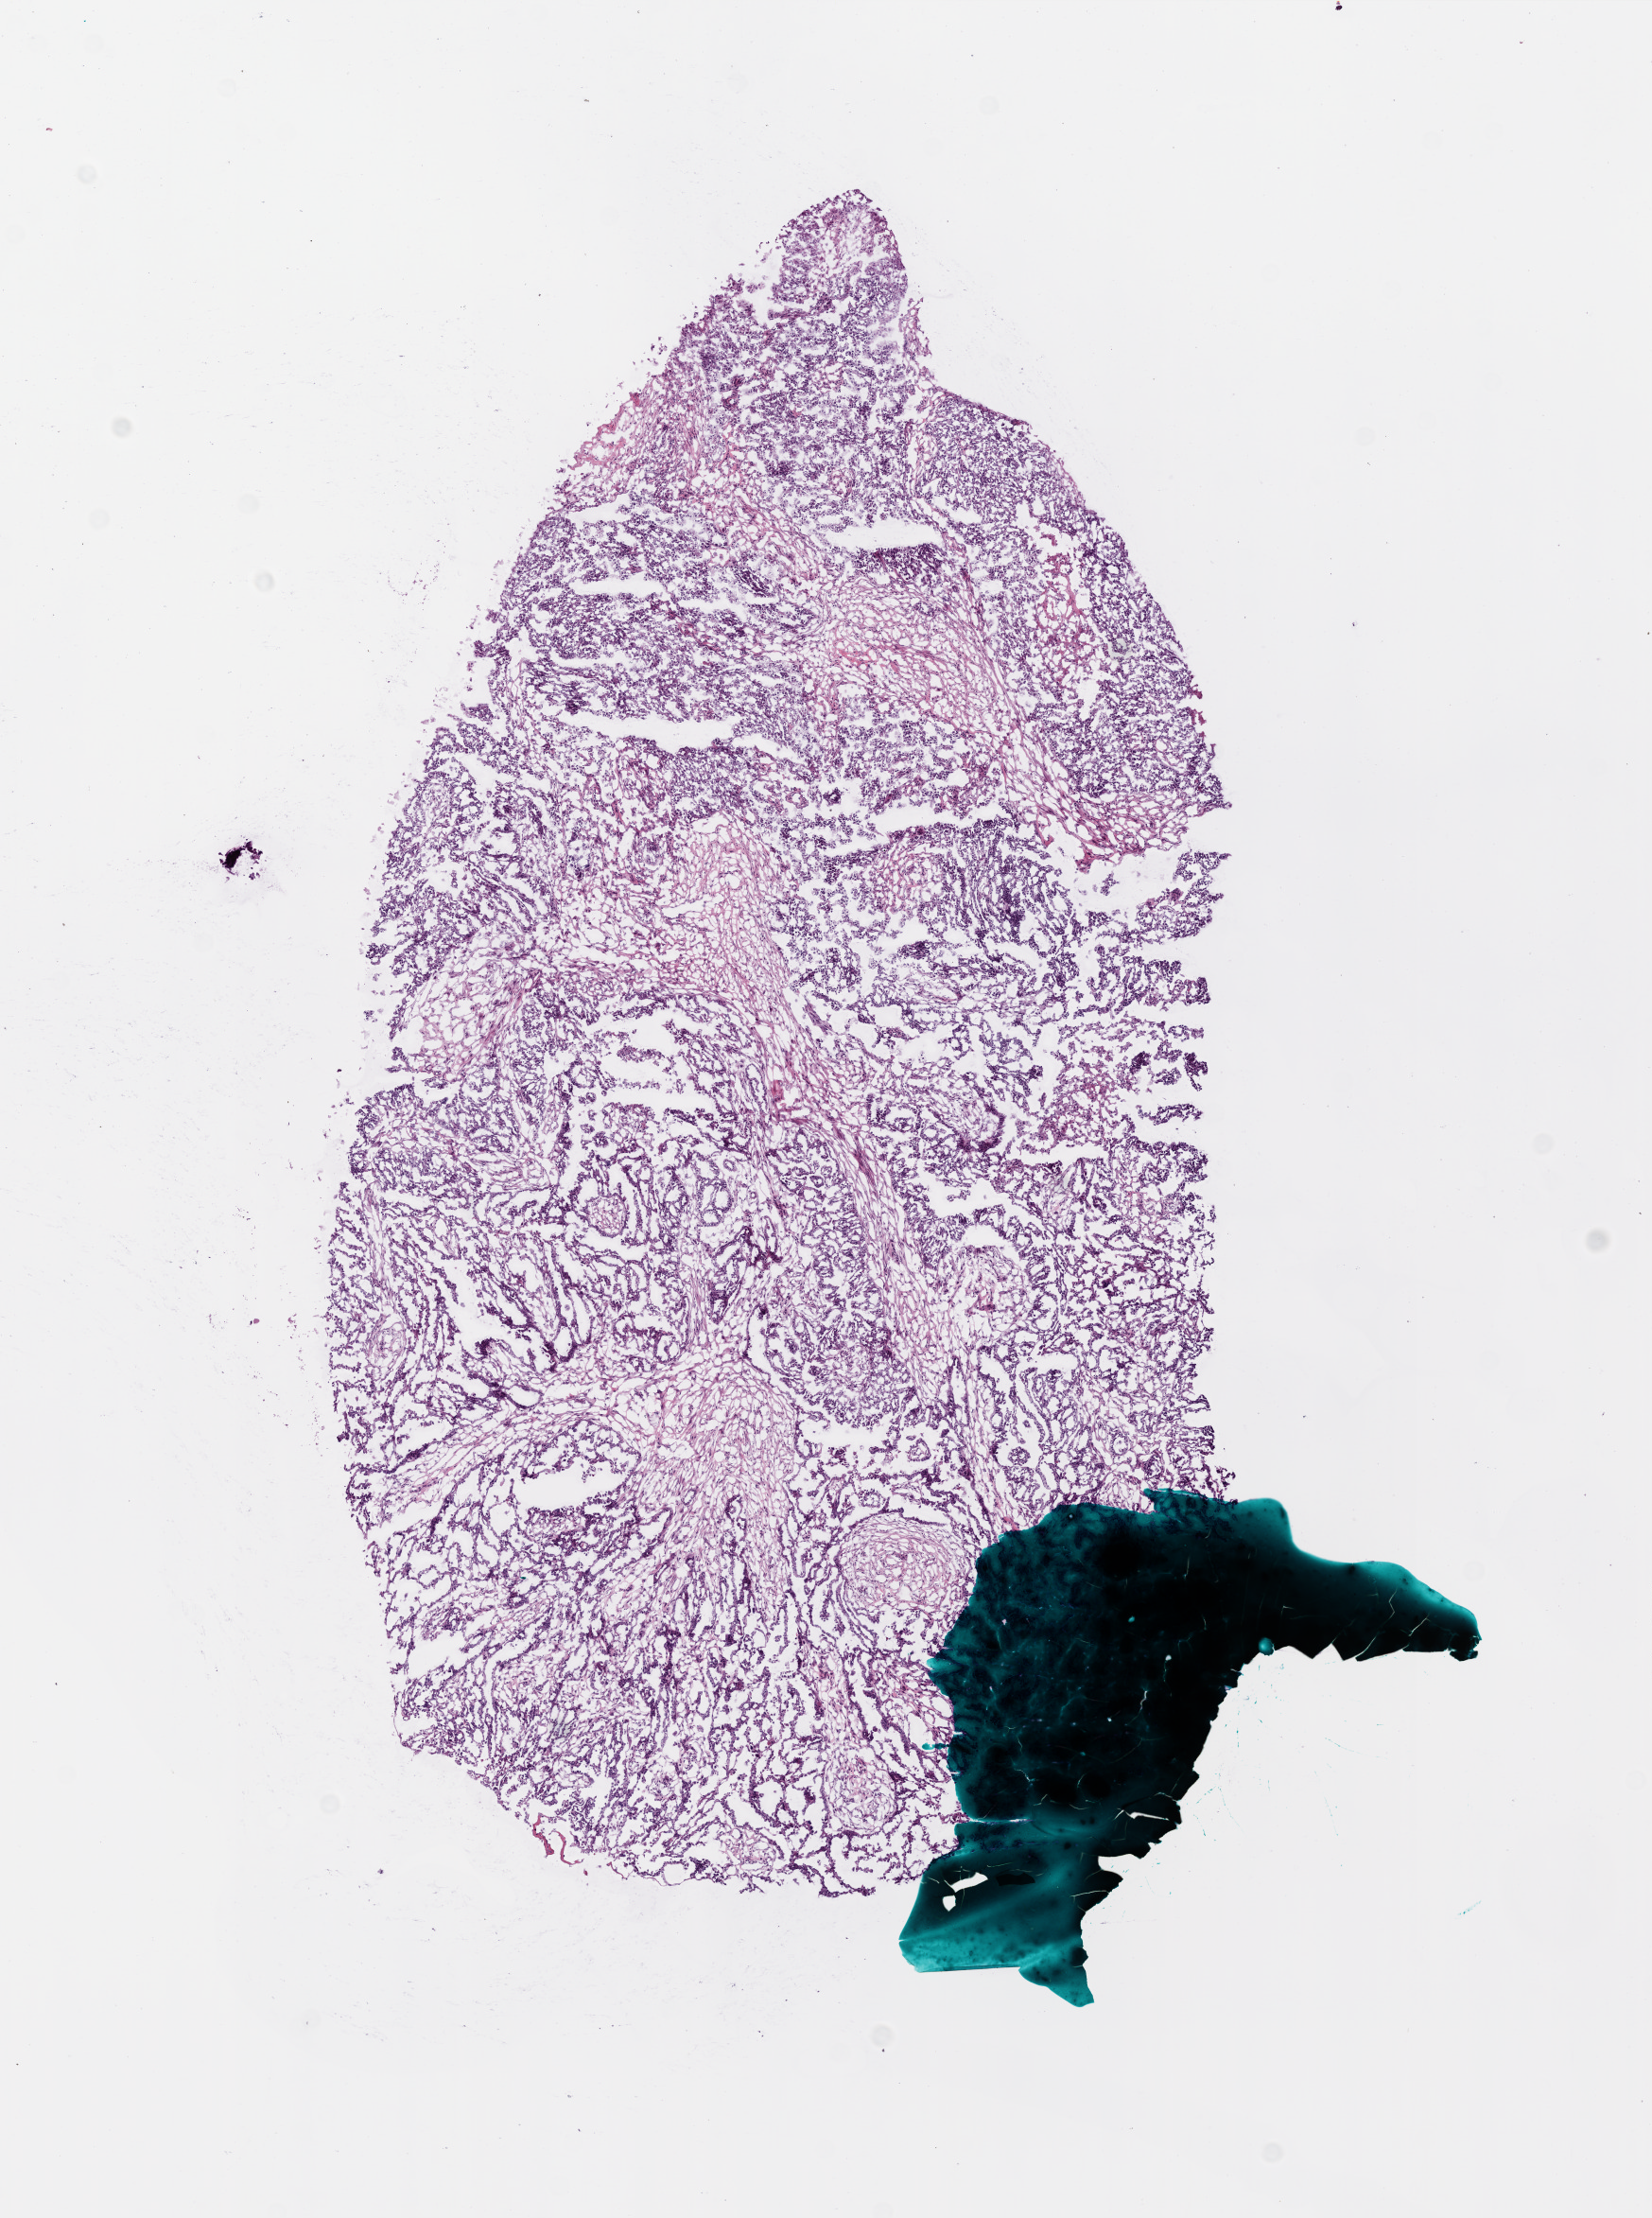
Whole-slide histology image, H&E, a low-resolution overview of the entire scanned area, about 7.0 x 9.4 mm. Frozen section from the bottom of the tissue portion. Ovary, primary tumour sample. Female, age 45 years at initial diagnosis. Histologic grade: G3 (poorly differentiated). Slide review estimates, as recorded: tumour nuclei 80%, normal cells 0%, necrosis 5%.
FIGO stage: IIIC. Histologic diagnosis: Serous cystadenocarcinoma, NOS.